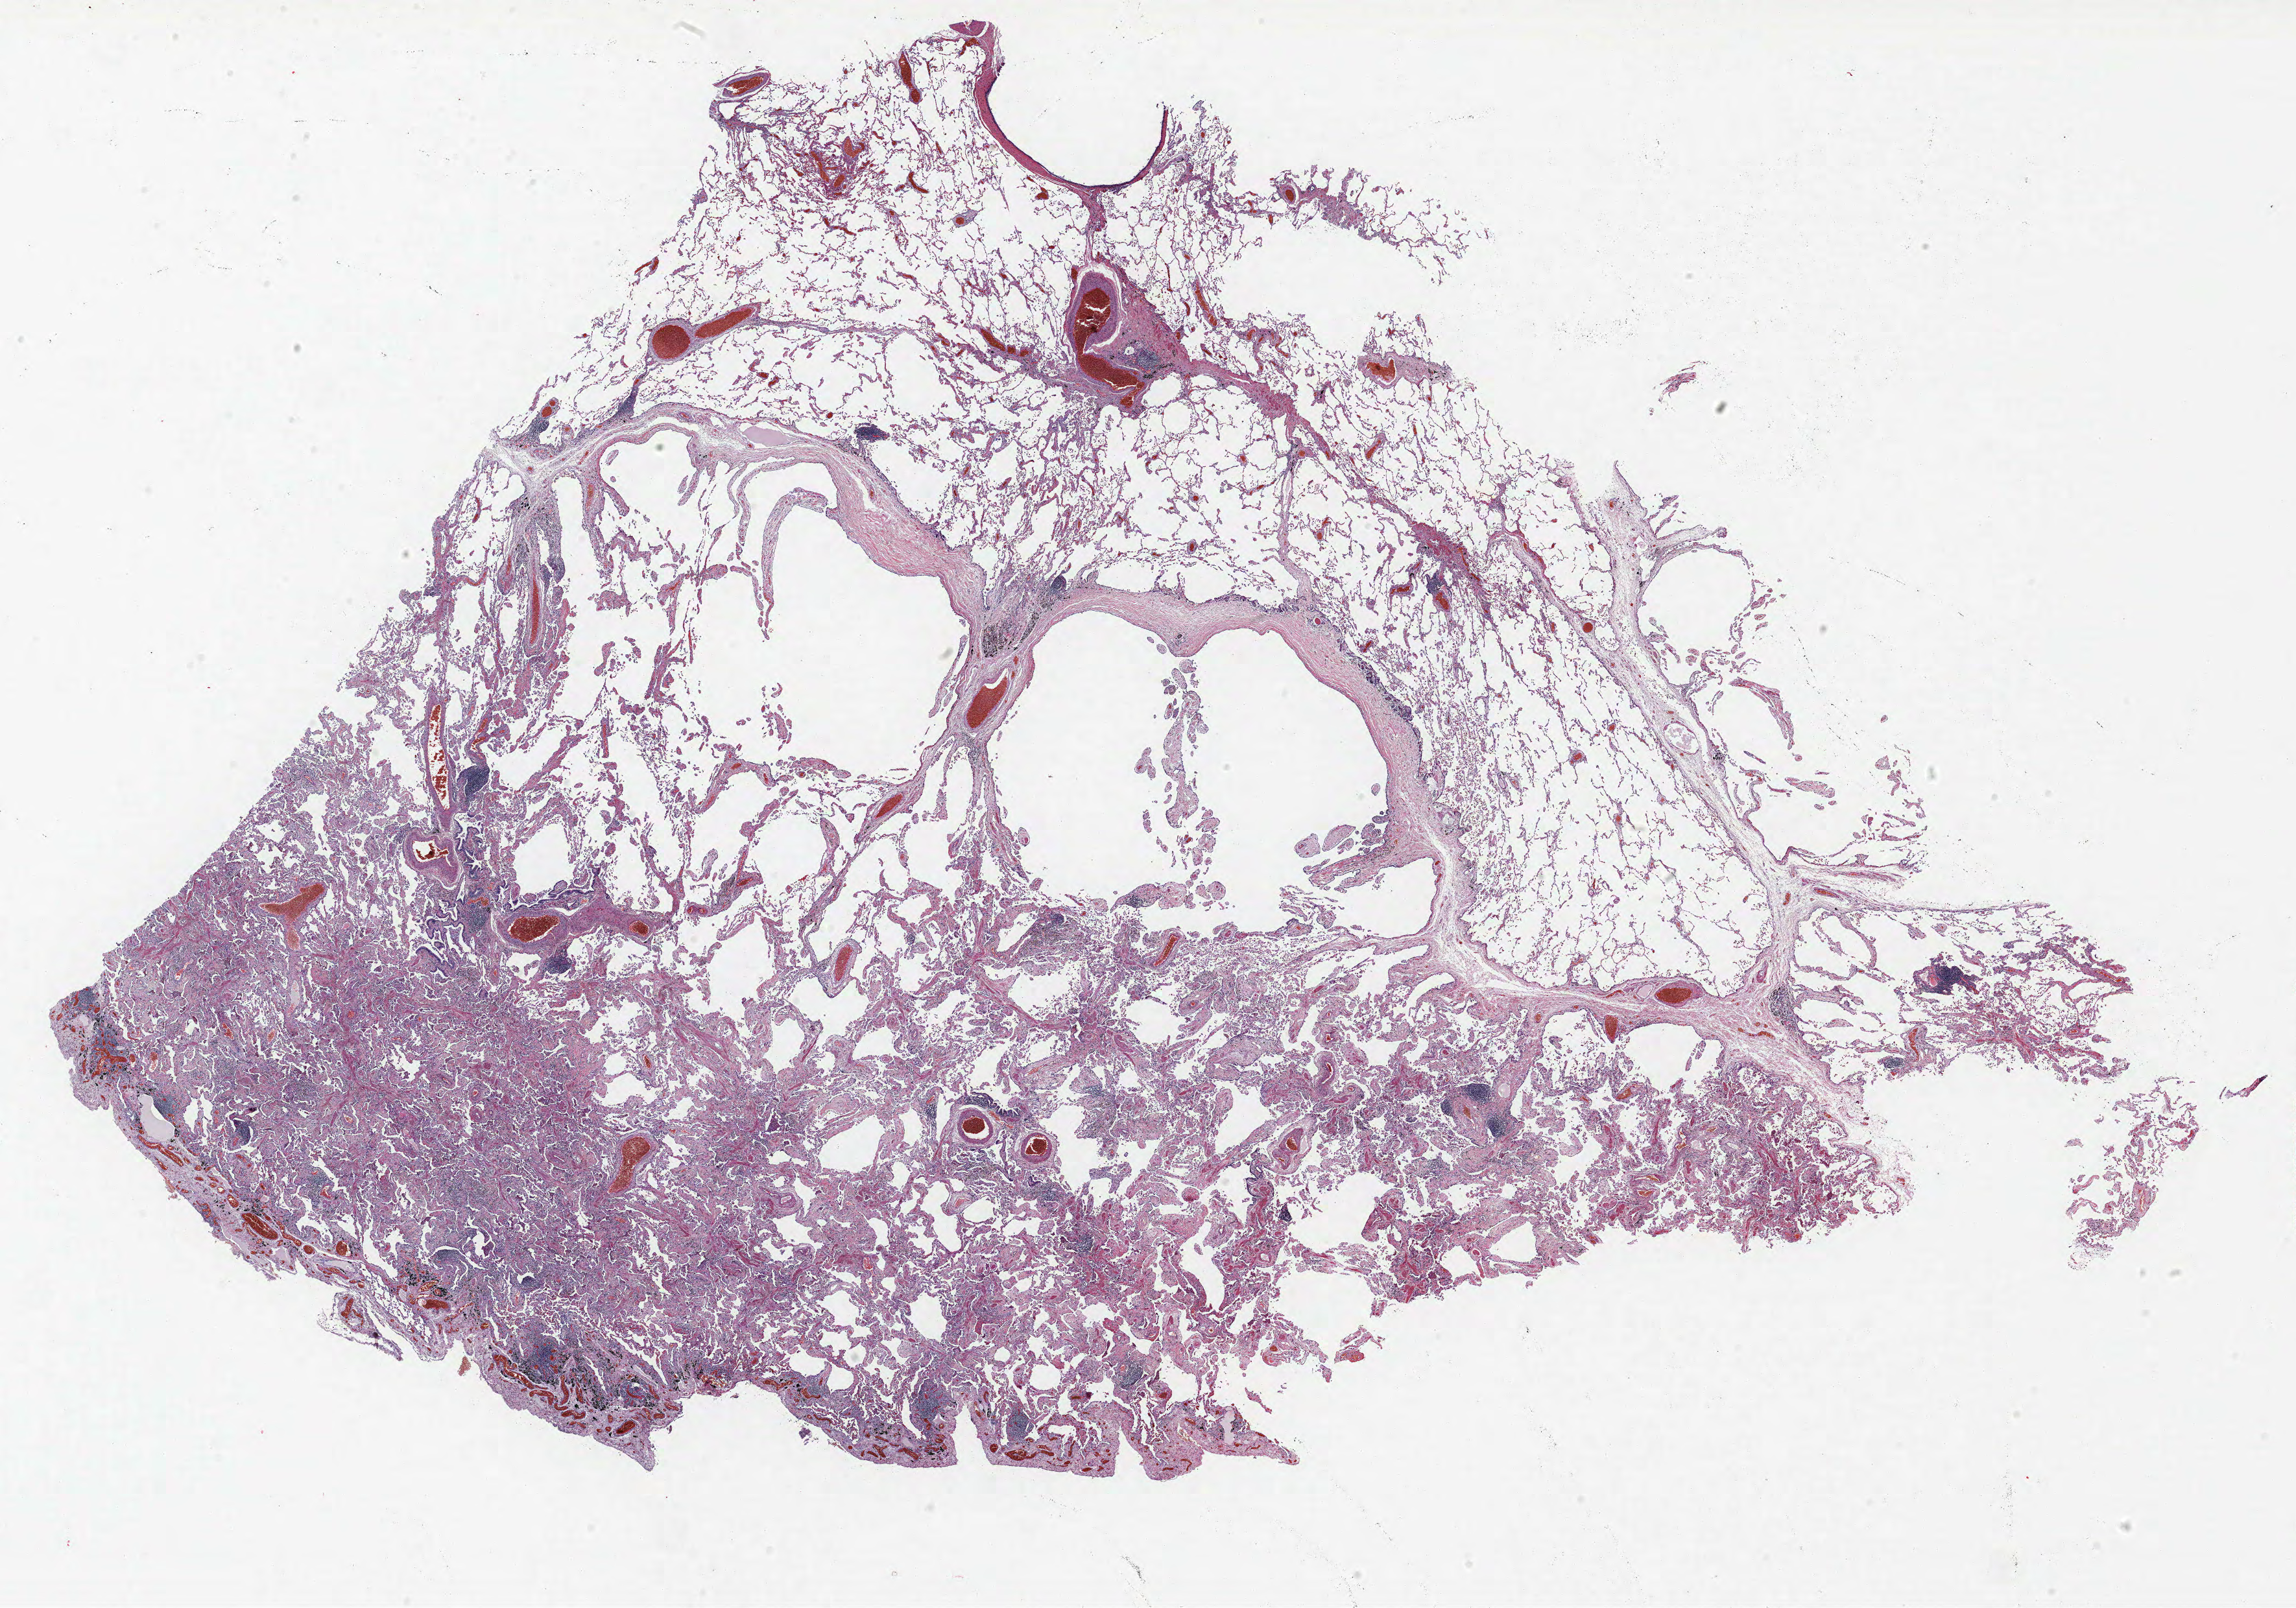
Whole-slide histology image, H&E-stained, low-resolution overview of the scanned area, about 28.3 x 19.8 mm, formalin-fixed paraffin-embedded (FFPE) section, lung. Male, age 71 at enrolment. Current smoker at enrolment.
Participant's lung-cancer diagnosis: Adenocarcinoma, NOS (ICD-O-3 8140/3).